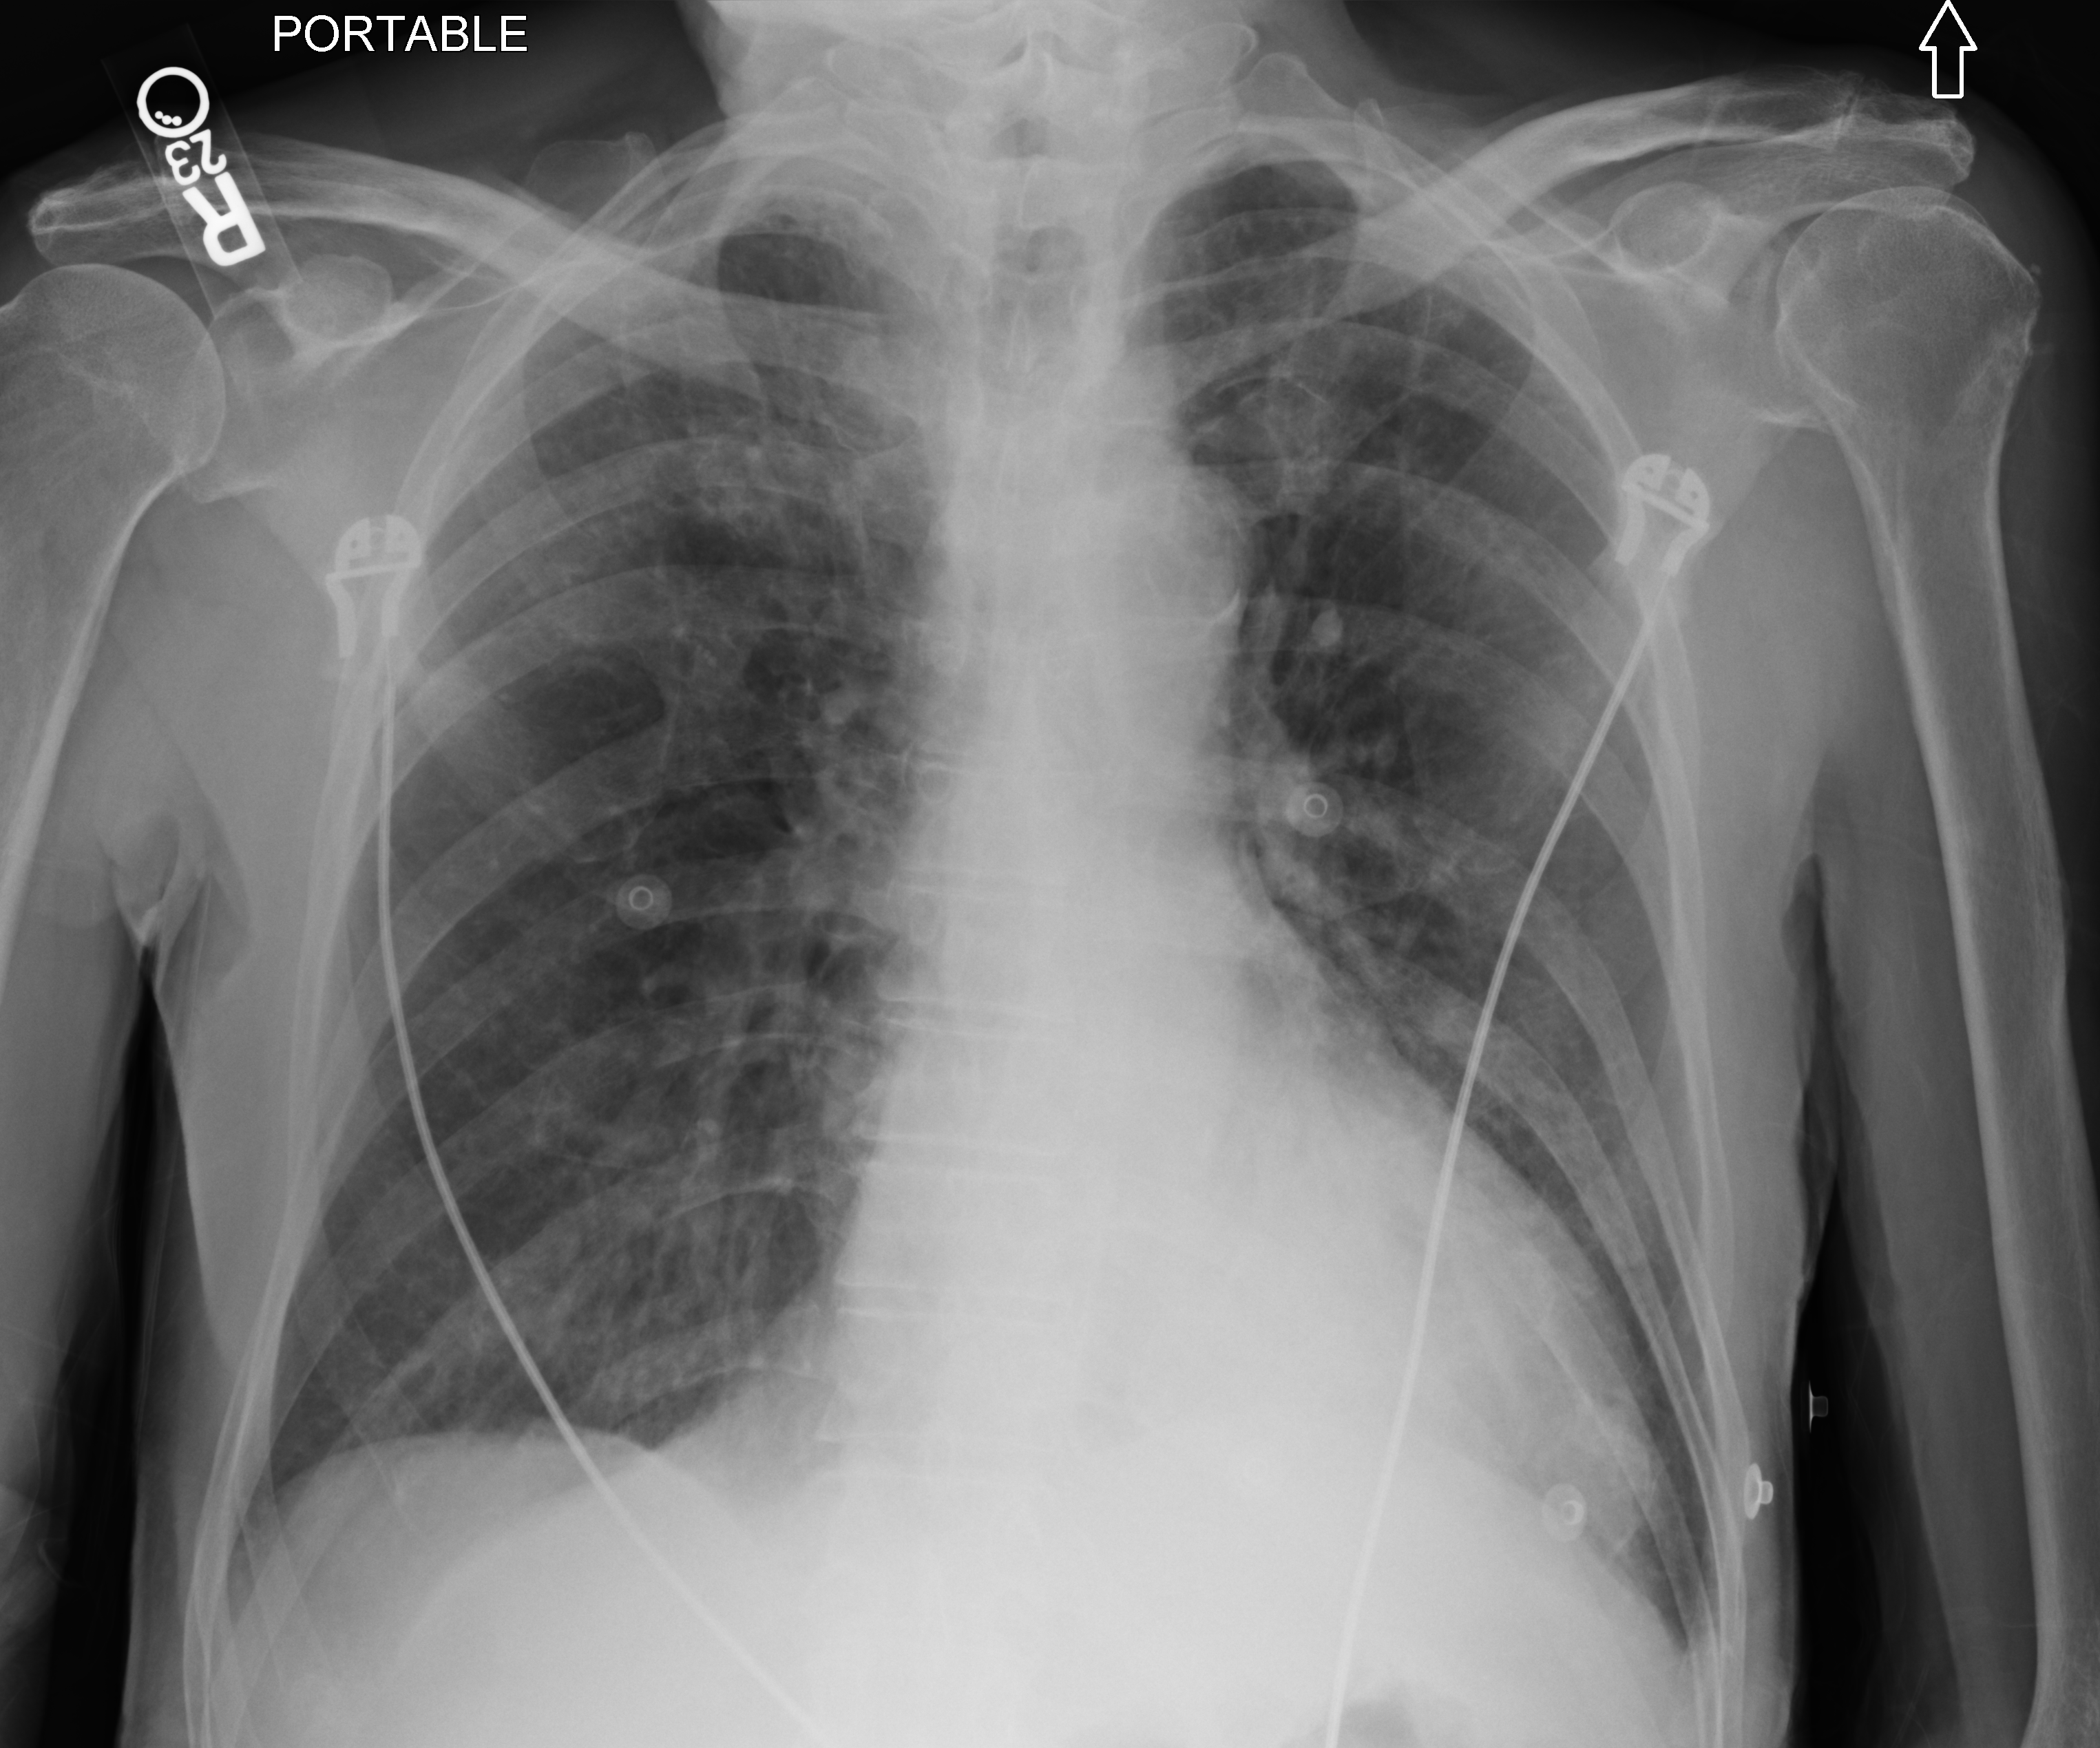
Bedside chest radiograph (computed radiography); anteroposterior (AP) projection. Patient hospitalised with COVID-19; male, aged 75–90 years.
Admission-level facts for this patient (not findings on this image; timing relative to this image not recorded): admitted to intensive care during this hospital stay: no.